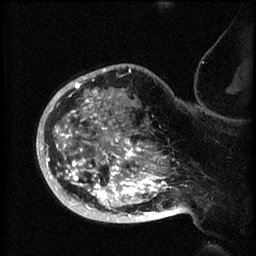
Breast MRI (dynamic contrast-enhanced), one sagittal slice; position 48 of 60 along the scan axis; 3 images stored at this slice position (order not interpretable as contrast timing); 1.5 T; TE 4.2 ms, TR 8.2 ms; 2 mm slice thickness; 256 × 256 image matrix. Female patient, age 50 years.
Outlined on this slice (semi-automatically segmented with operator editing):
- analysis volume of interest (the breast-tissue region the enhancement analysis was run in; not a lesion): bounding box <44,72,173,219> (left, top, right, bottom; pixels)
- tumour enhancement mask (voxels above the 70 % enhancement threshold inside the analysis volume of interest): <44,72,173,219>